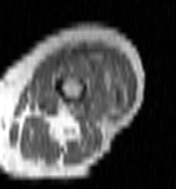
MRI of an extremity soft-tissue mass, one axial slice. Slice 34 of 100 in the series (ordered by position). MR volume resampled by the dataset authors to the PET/CT grid (not the native acquisition matrix). 3.27 mm slice thickness. 176 × 189 image matrix. Female patient. Case-level facts recorded for this patient, not image findings: histological type: undifferentiated – high grade; grade: high; site of the primary tumour: left thigh.
Structures marked on this image (expert contour drawn on MRI and transferred to this co-registered scan by the dataset authors):
- gross tumour volume including surrounding oedema: bounding box (x1, y1, x2, y2) in pixels: (62, 52, 125, 115)